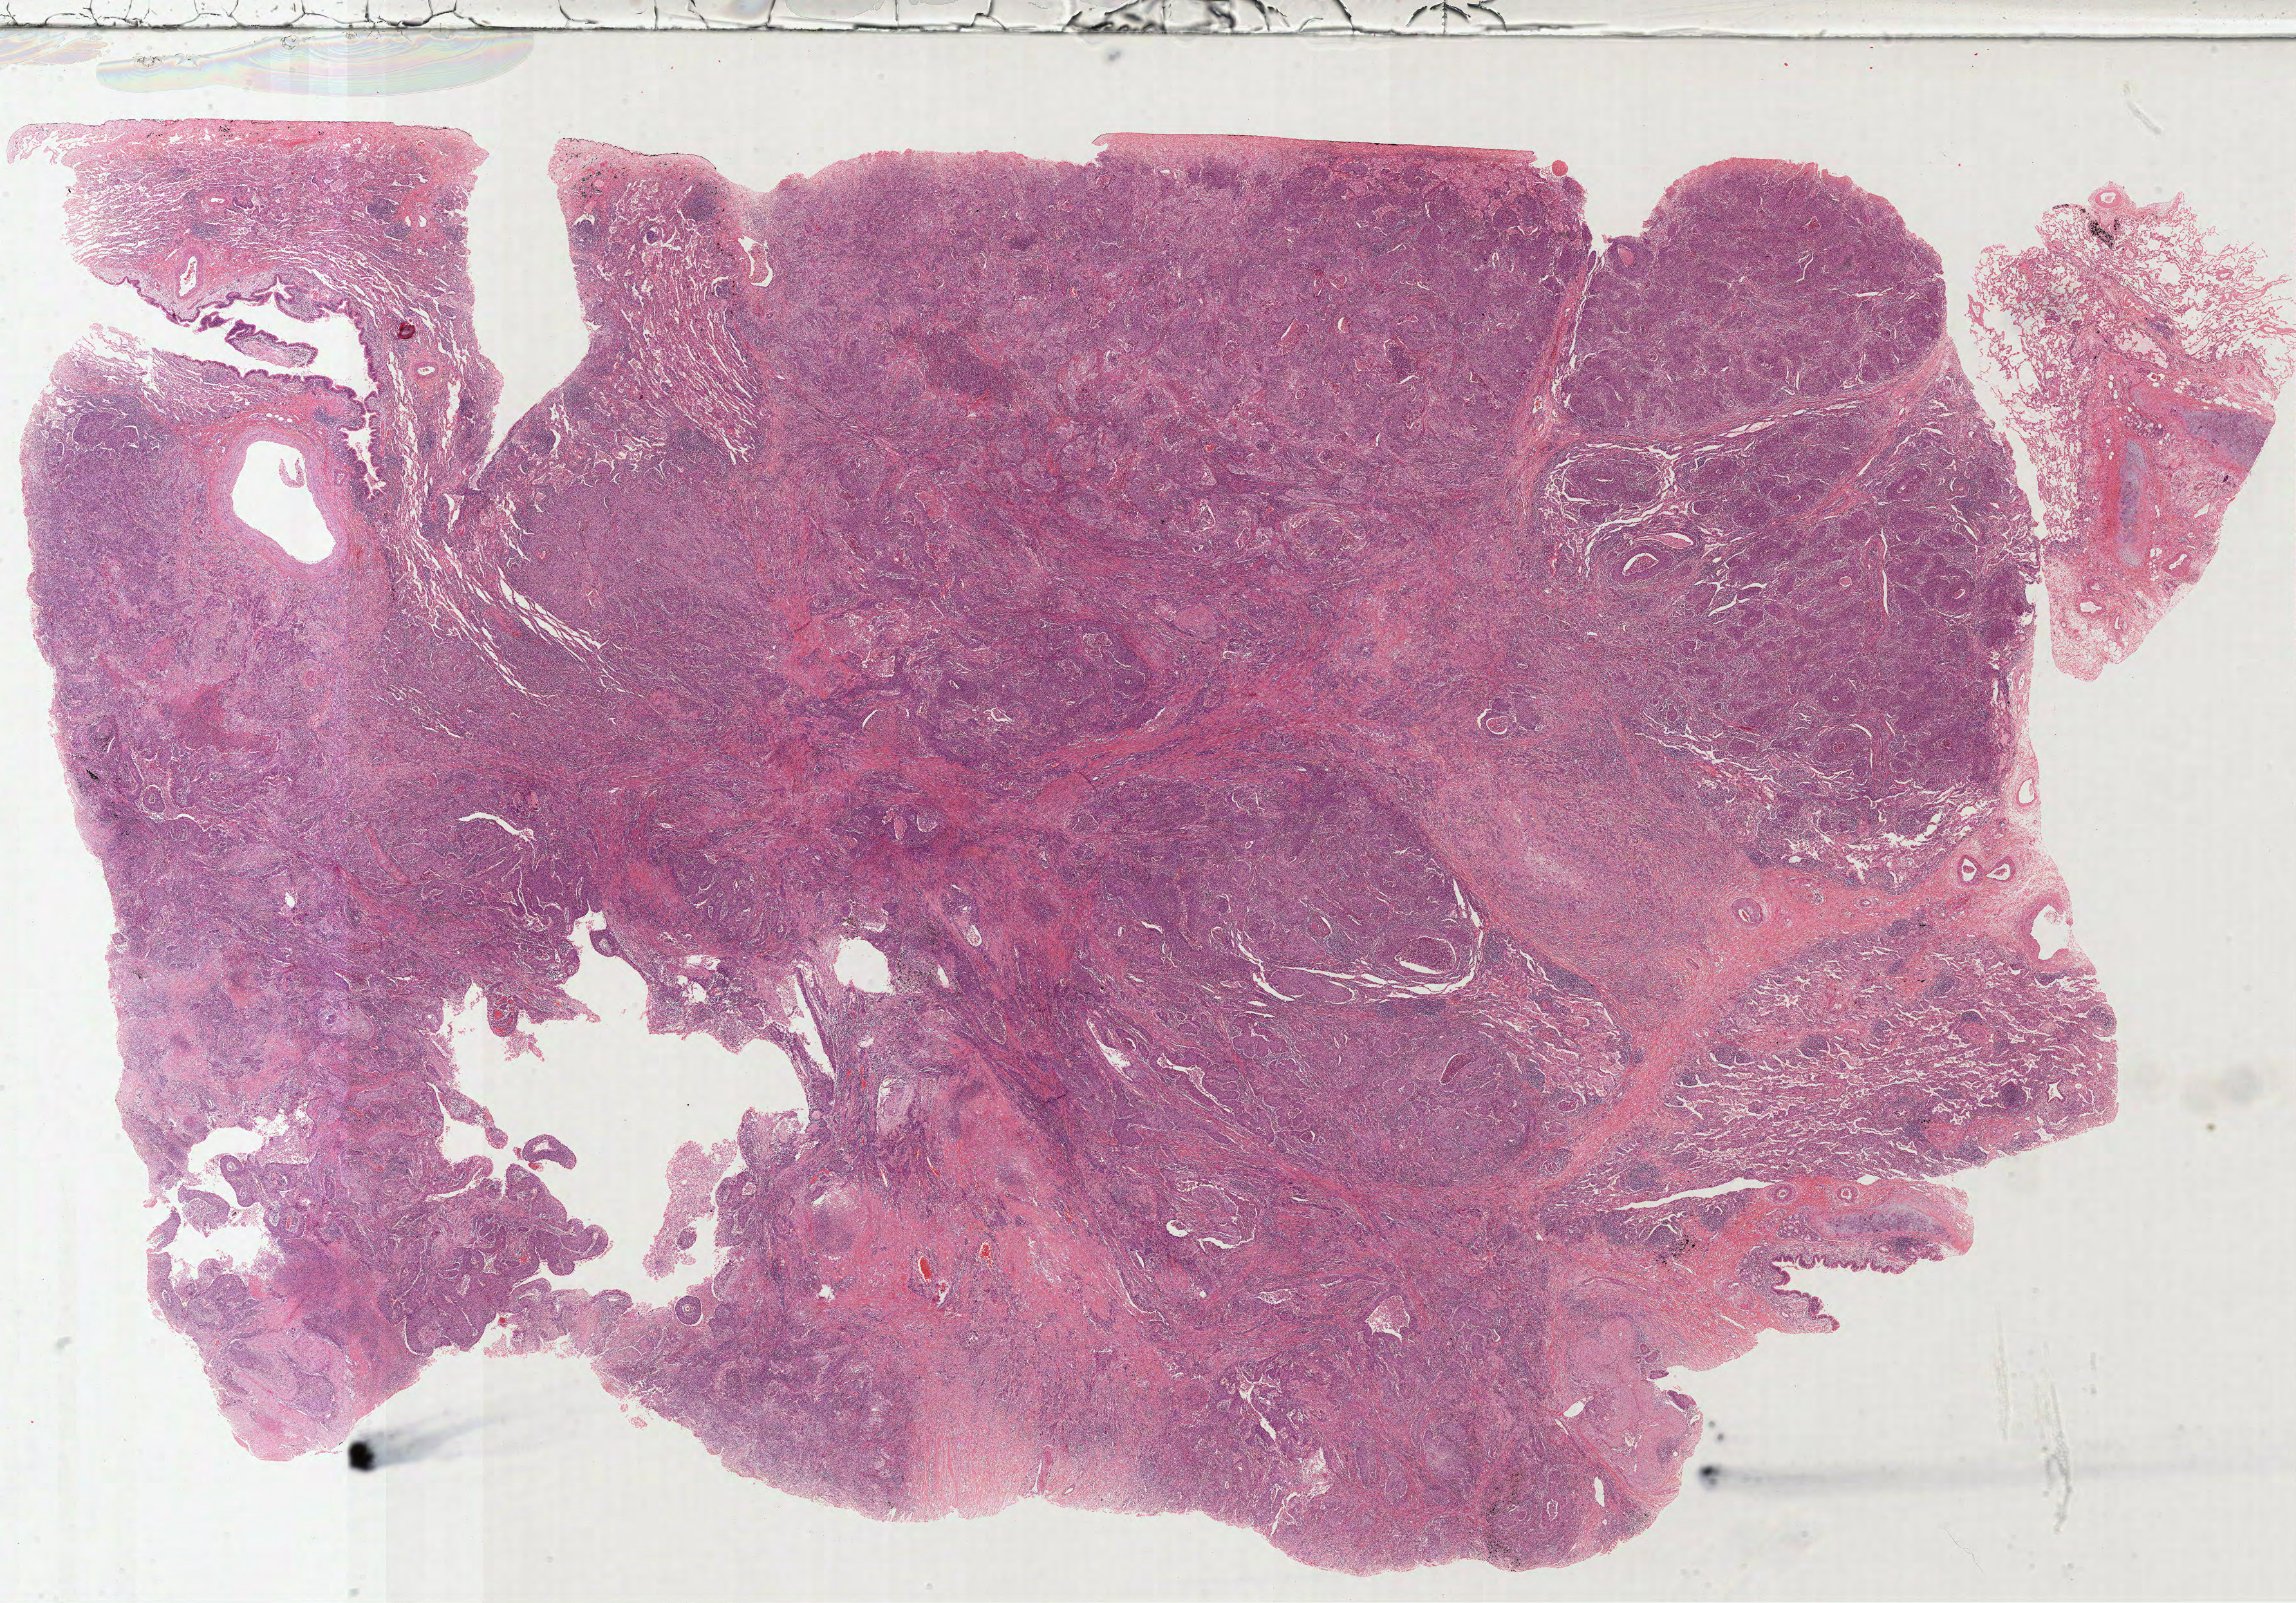
Digitized Hematoxylin and eosin (H&E) stained tissue section (whole slide) — a low-resolution overview of the entire scanned area, about 28.8 x 20.1 mm (from a 40x scan); formalin-fixed paraffin-embedded (FFPE) diagnostic section; sample: primary tumour, lung. Patient: female, age at initial diagnosis 74 years.
Pathologic diagnosis: Squamous cell carcinoma, NOS.